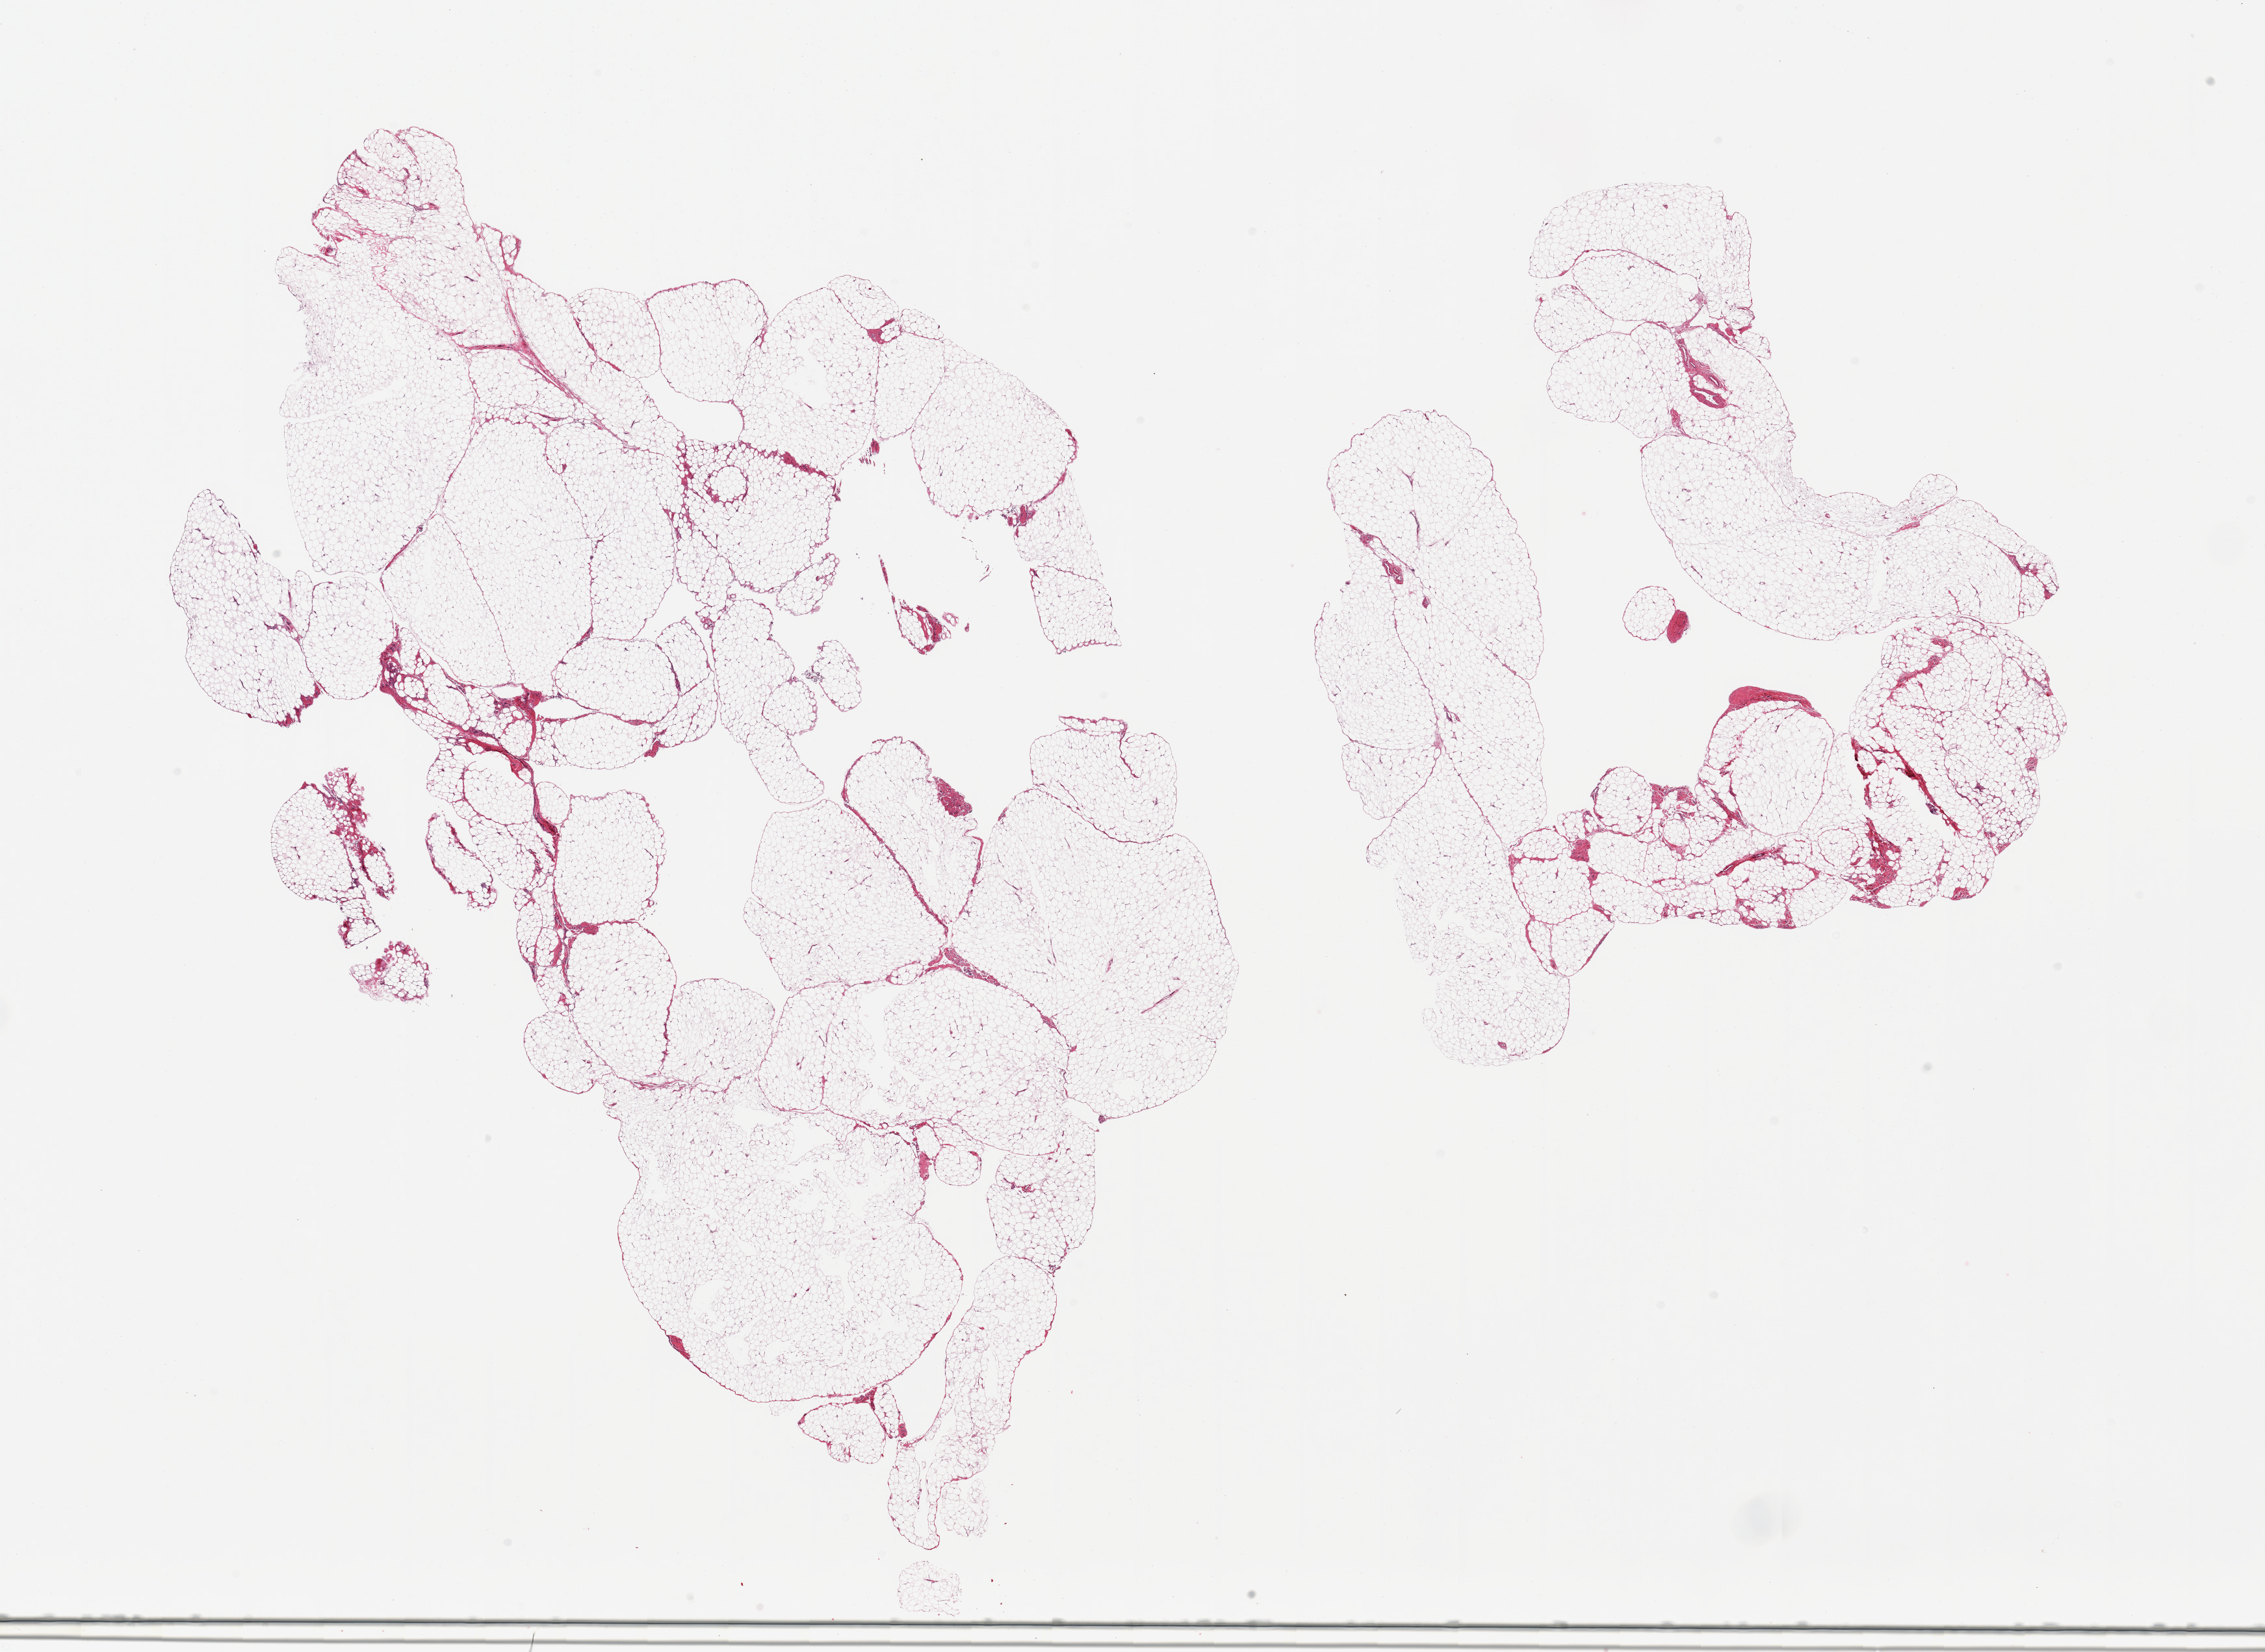
Whole-slide image, hematoxylin and eosin (H&E) stain, shown as a low-resolution overview of the whole scanned area (about 27.6 x 20.1 mm), PAXgene-fixed paraffin-embedded (PFPE) section, section of omentum (target tissue), donor tissue sample. Male donor.
Pathologist's review note for this sample: 2 pieces; no fibrous content.